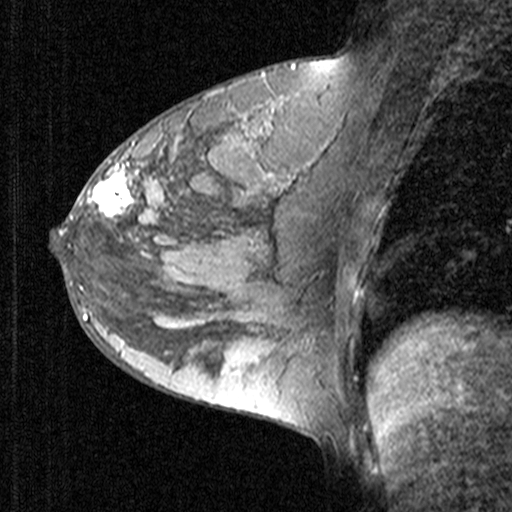
Breast MRI (dynamic contrast-enhanced), one sagittal slice; slice 23 of 44 in the series (ordered by position); dynamic contrast-enhanced study with each time point stored as its own series, time point 2 of 3 at this slice position (early post-contrast, ordered by acquisition time); 1.5 T; TE 4.5 ms, TR 11 ms; 3 mm slice thickness; 512 × 512 image matrix, field of view 200 × 200 mm. Female patient, age 27 years. Case-level facts recorded for this patient, not image findings: setting: breast cancer imaged before/during neoadjuvant chemotherapy; receptor status: HR-positive, HER2-negative.
Annotated regions visible in this slice (semi-automatically segmented with operator editing):
- analysis volume of interest (the breast-tissue region the enhancement analysis was run in; not a lesion): bounding box (x1, y1, x2, y2) in pixels: (68, 146, 165, 239)
- tumour enhancement mask (voxels above the 90 % enhancement threshold inside the analysis volume of interest): (71, 175, 132, 219)